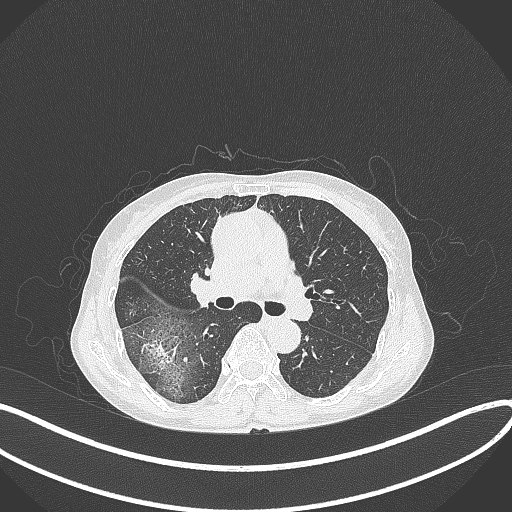
Chest CT, one axial slice. Slice 237 of 371 in the series (ordered by position). Reconstruction kernel B70f. Lung window (W 1500 / L -600 HU). 1 mm slice thickness. 512 × 512 image matrix, field of view 400 × 400 mm. Female patient, age 69 years. Case-level facts recorded for this patient, not image findings: clinical TNM (as recorded): T1b N0 M0; histopathological grade: G2-3.
Annotated regions visible in this slice (bounding box drawn by a radiologist):
- lung tumour (recorded histology: adenocarcinoma): bounding box <143,332,183,366> (left, top, right, bottom; pixels)